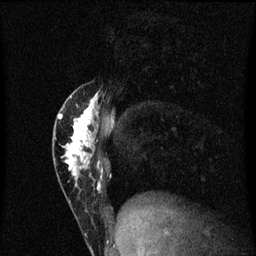
Breast MRI (dynamic contrast-enhanced), one sagittal slice; position 21 of 60 along the scan axis; dynamic contrast-enhanced series, image 2 of 3 at this slice position (ordered by acquisition); 1.5 T; TE 4.2 ms, TR 8.4 ms; 256 × 256 image matrix. Patient: female, 40 years.
Outlined on this slice (semi-automatically segmented with operator editing):
- analysis volume of interest (the breast-tissue region the enhancement analysis was run in; not a lesion): bounding box [x1, y1, x2, y2] px = [54, 84, 105, 203]
- tumour enhancement mask (voxels above the 70 % enhancement threshold inside the analysis volume of interest): [58, 94, 104, 181]